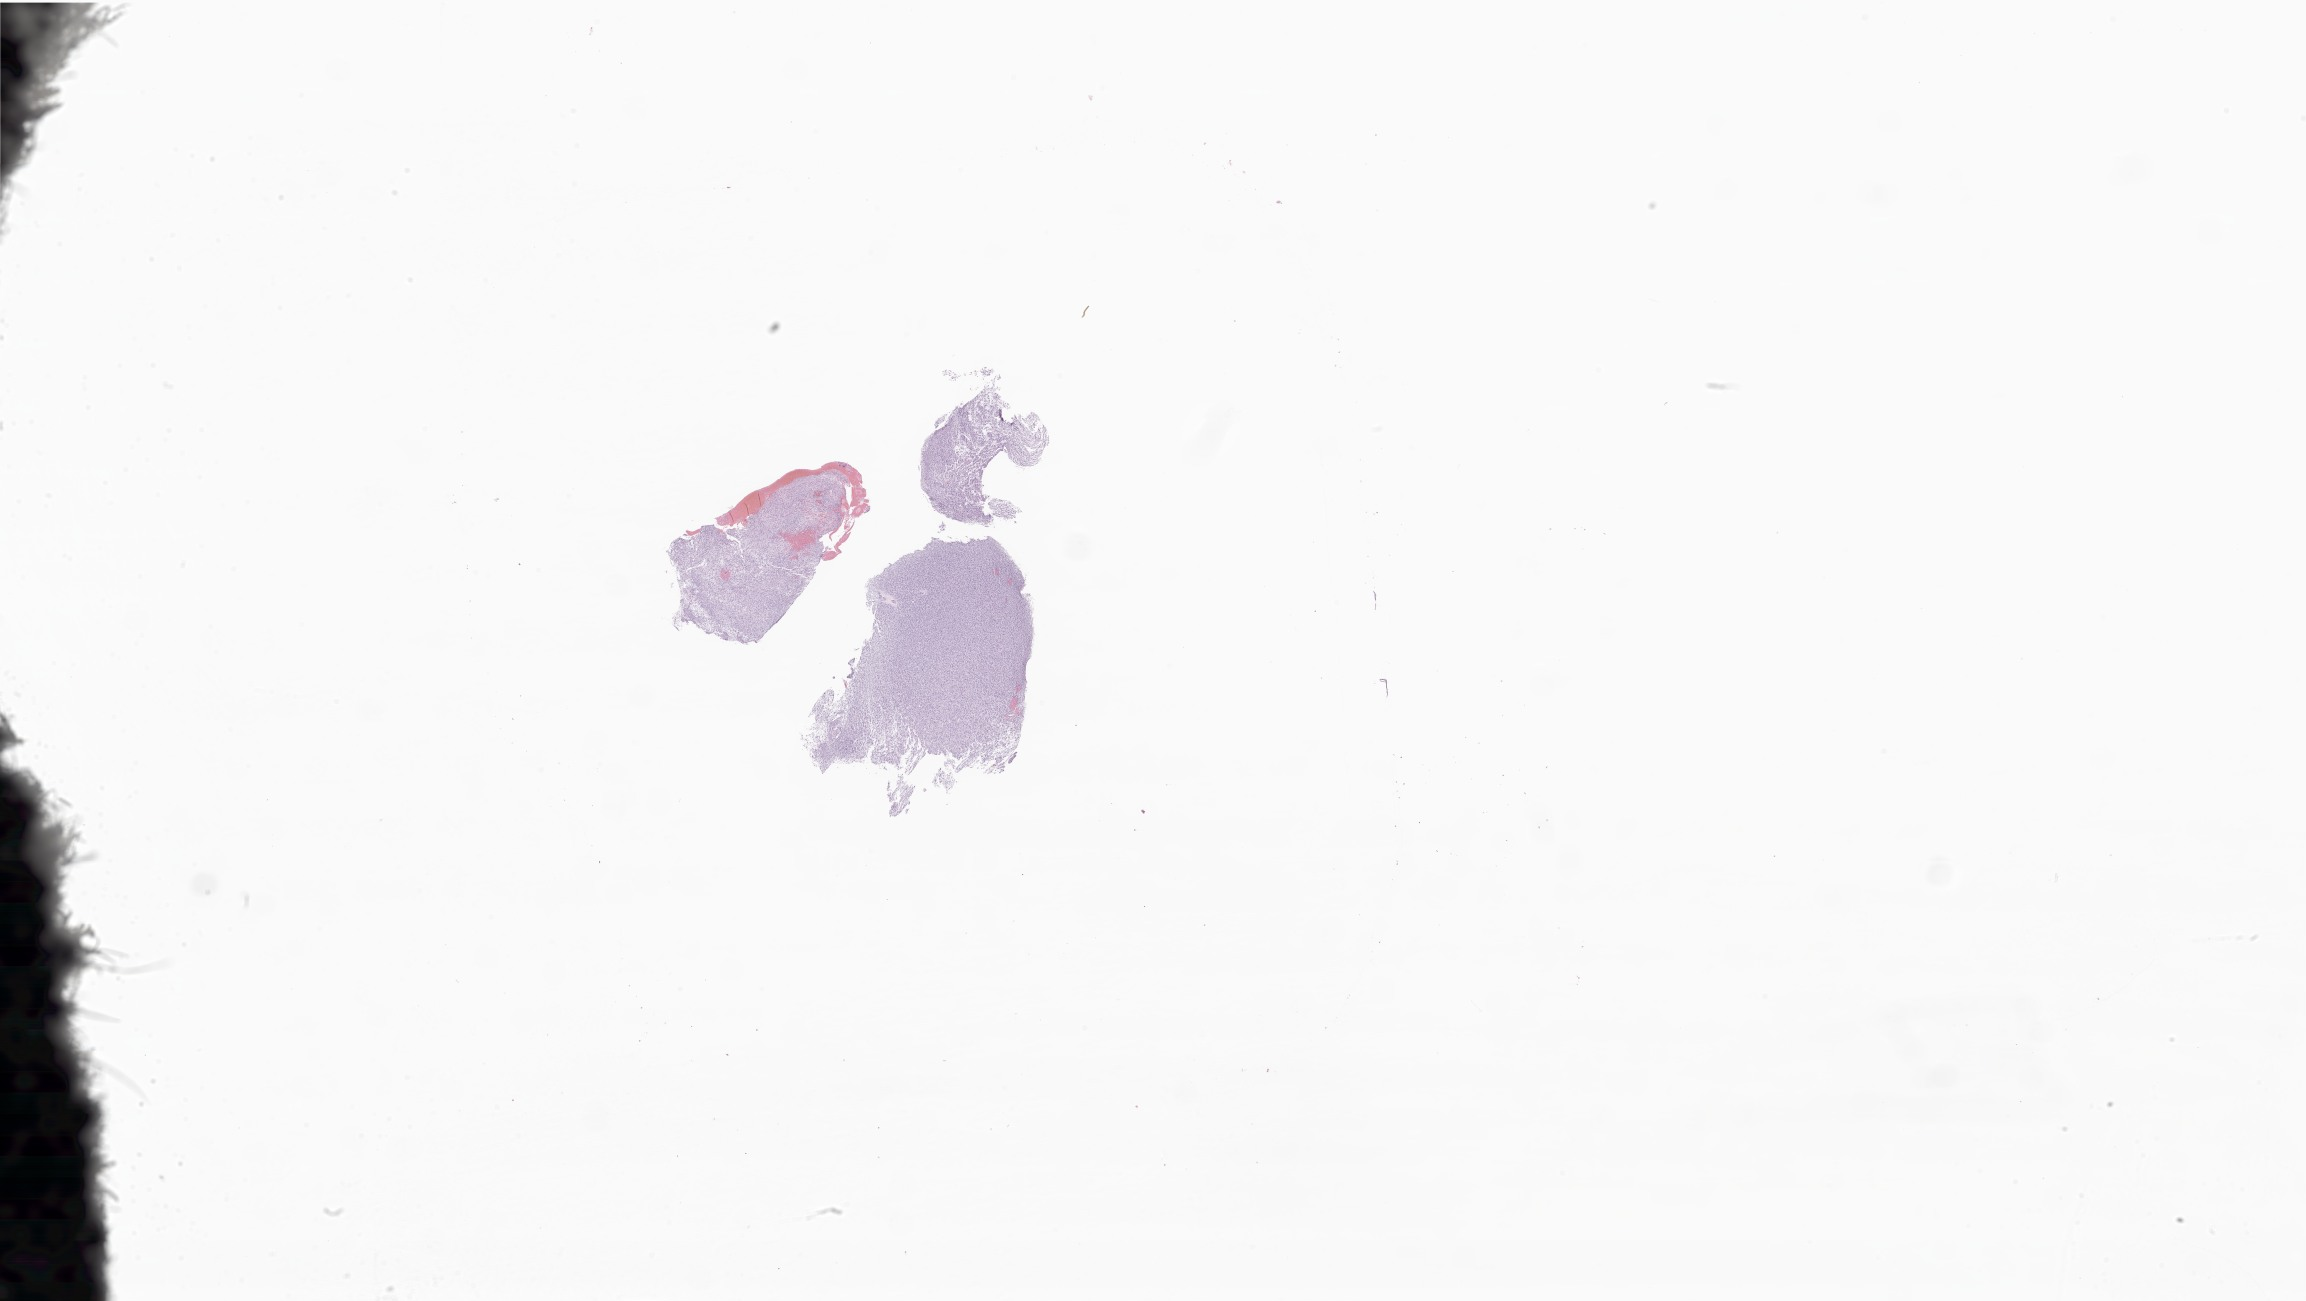
Whole-slide image, H&E stain of tumor tissue from the brain stem — shown as a low-resolution overview of the whole scanned area (about 38.9 x 21.9 mm). Formalin-fixed, paraffin-embedded (FFPE) tissue. Patient: male, age 52 months (4 years 4 months).
Recorded diagnosis: Glioma, malignant.